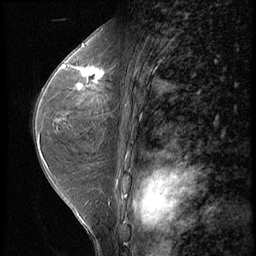
Breast MRI (dynamic contrast-enhanced), one sagittal slice. Position 33 of 56 along the scan axis. 3 images stored at this slice position (order not interpretable as contrast timing). 1.5 T. TE 4.2 ms, TR 9 ms. 2.5 mm slice thickness. 256 × 256 image matrix, field of view 180 × 180 mm. Female patient, age 44 years. From the clinical record (not read from this slice): setting: breast cancer imaged before/during neoadjuvant chemotherapy; receptor status: triple-negative.
Outlined on this slice (semi-automatically segmented with operator editing):
- analysis volume of interest (the breast-tissue region the enhancement analysis was run in; not a lesion): box from (x=71, y=54) to (x=112, y=99) px
- tumour enhancement mask (voxels above the 140 % enhancement threshold inside the analysis volume of interest): (x=76, y=66)–(x=103, y=91)